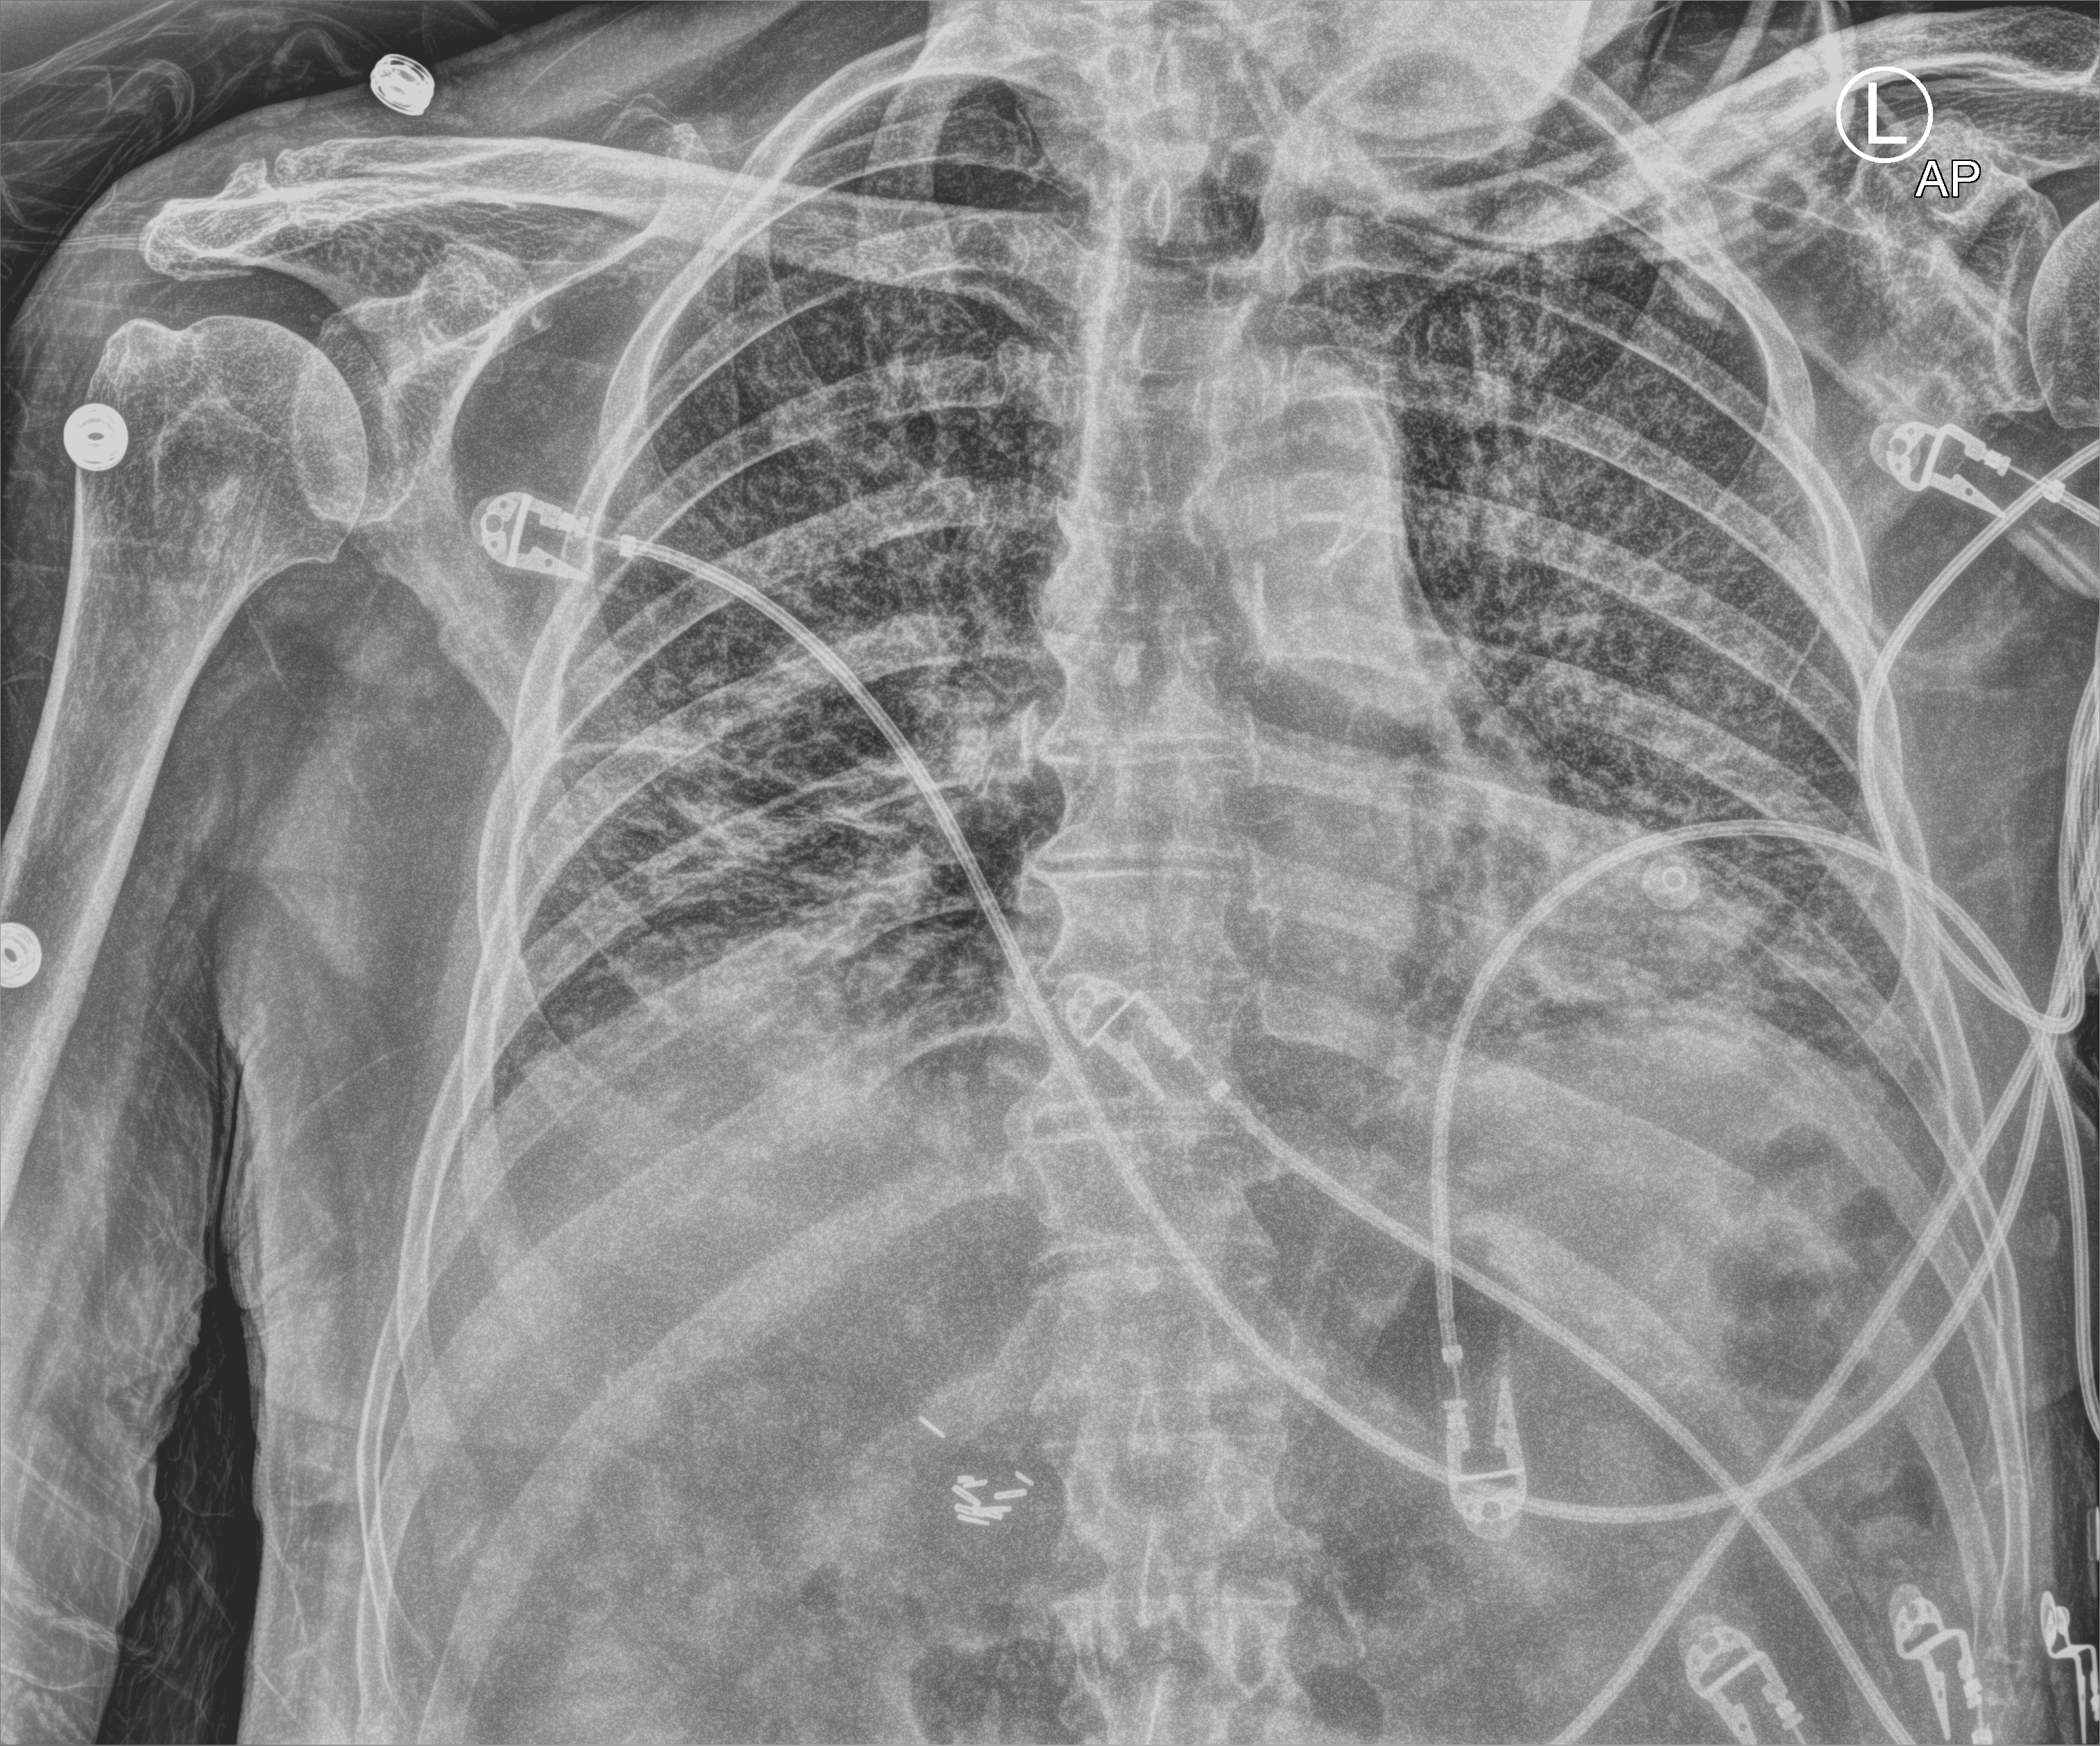
Chest X-ray (portable), anteroposterior (AP) projection. Patient hospitalised with COVID-19; male, aged 75–90 years.
From the hospital-stay record, not from the radiograph (when in the stay this image was taken is not recorded):
- diabetes (admission record): no
- hypertension (admission record): yes
- mechanically ventilated during this hospital stay: yes